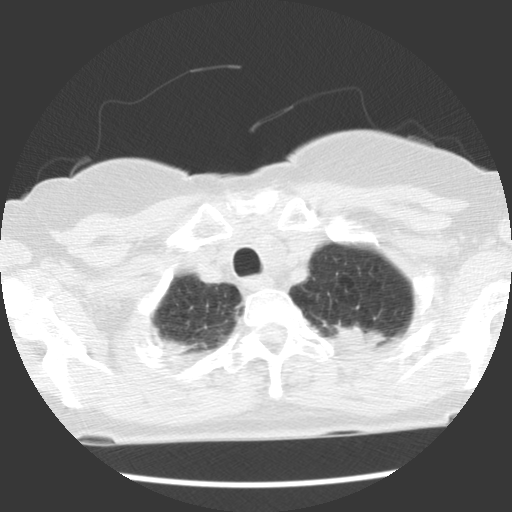
Low-dose screening chest CT, one axial slice; position 104 of 120 along the scan axis; lung window (W 1500 / L -600 HU); 2.5 mm slice thickness; 512 × 512 image matrix, field of view 300 × 300 mm.
Annotated regions visible in this slice (expert manual segmentation):
- lesion 1 (tumor, upper lobe of left lung): bounding box <333,323,387,348> (left, top, right, bottom; pixels)